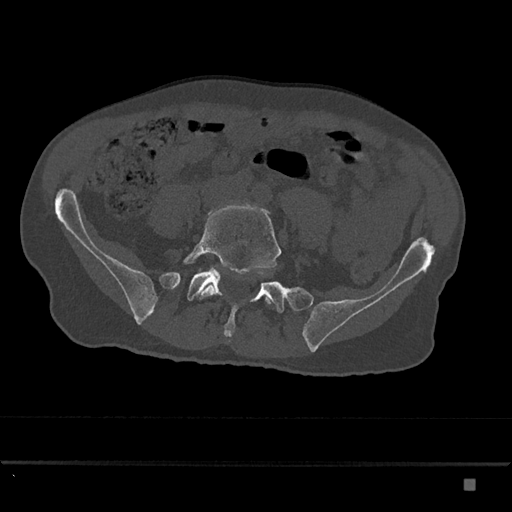
CT including the spine, one axial slice. Slice 260 of 797 in the series (ordered by position). Bone window (W 1800 / L 400 HU). 0.5 mm slice thickness. 512 × 512 image matrix. Patient: male, 72 years. Case-level facts recorded for this patient, not image findings: primary cancer: prostate.
Annotated regions visible in this slice (semi-automatically segmented with operator editing):
- L5 vertebra: bounding box [x1, y1, x2, y2] px = [183, 205, 282, 305]